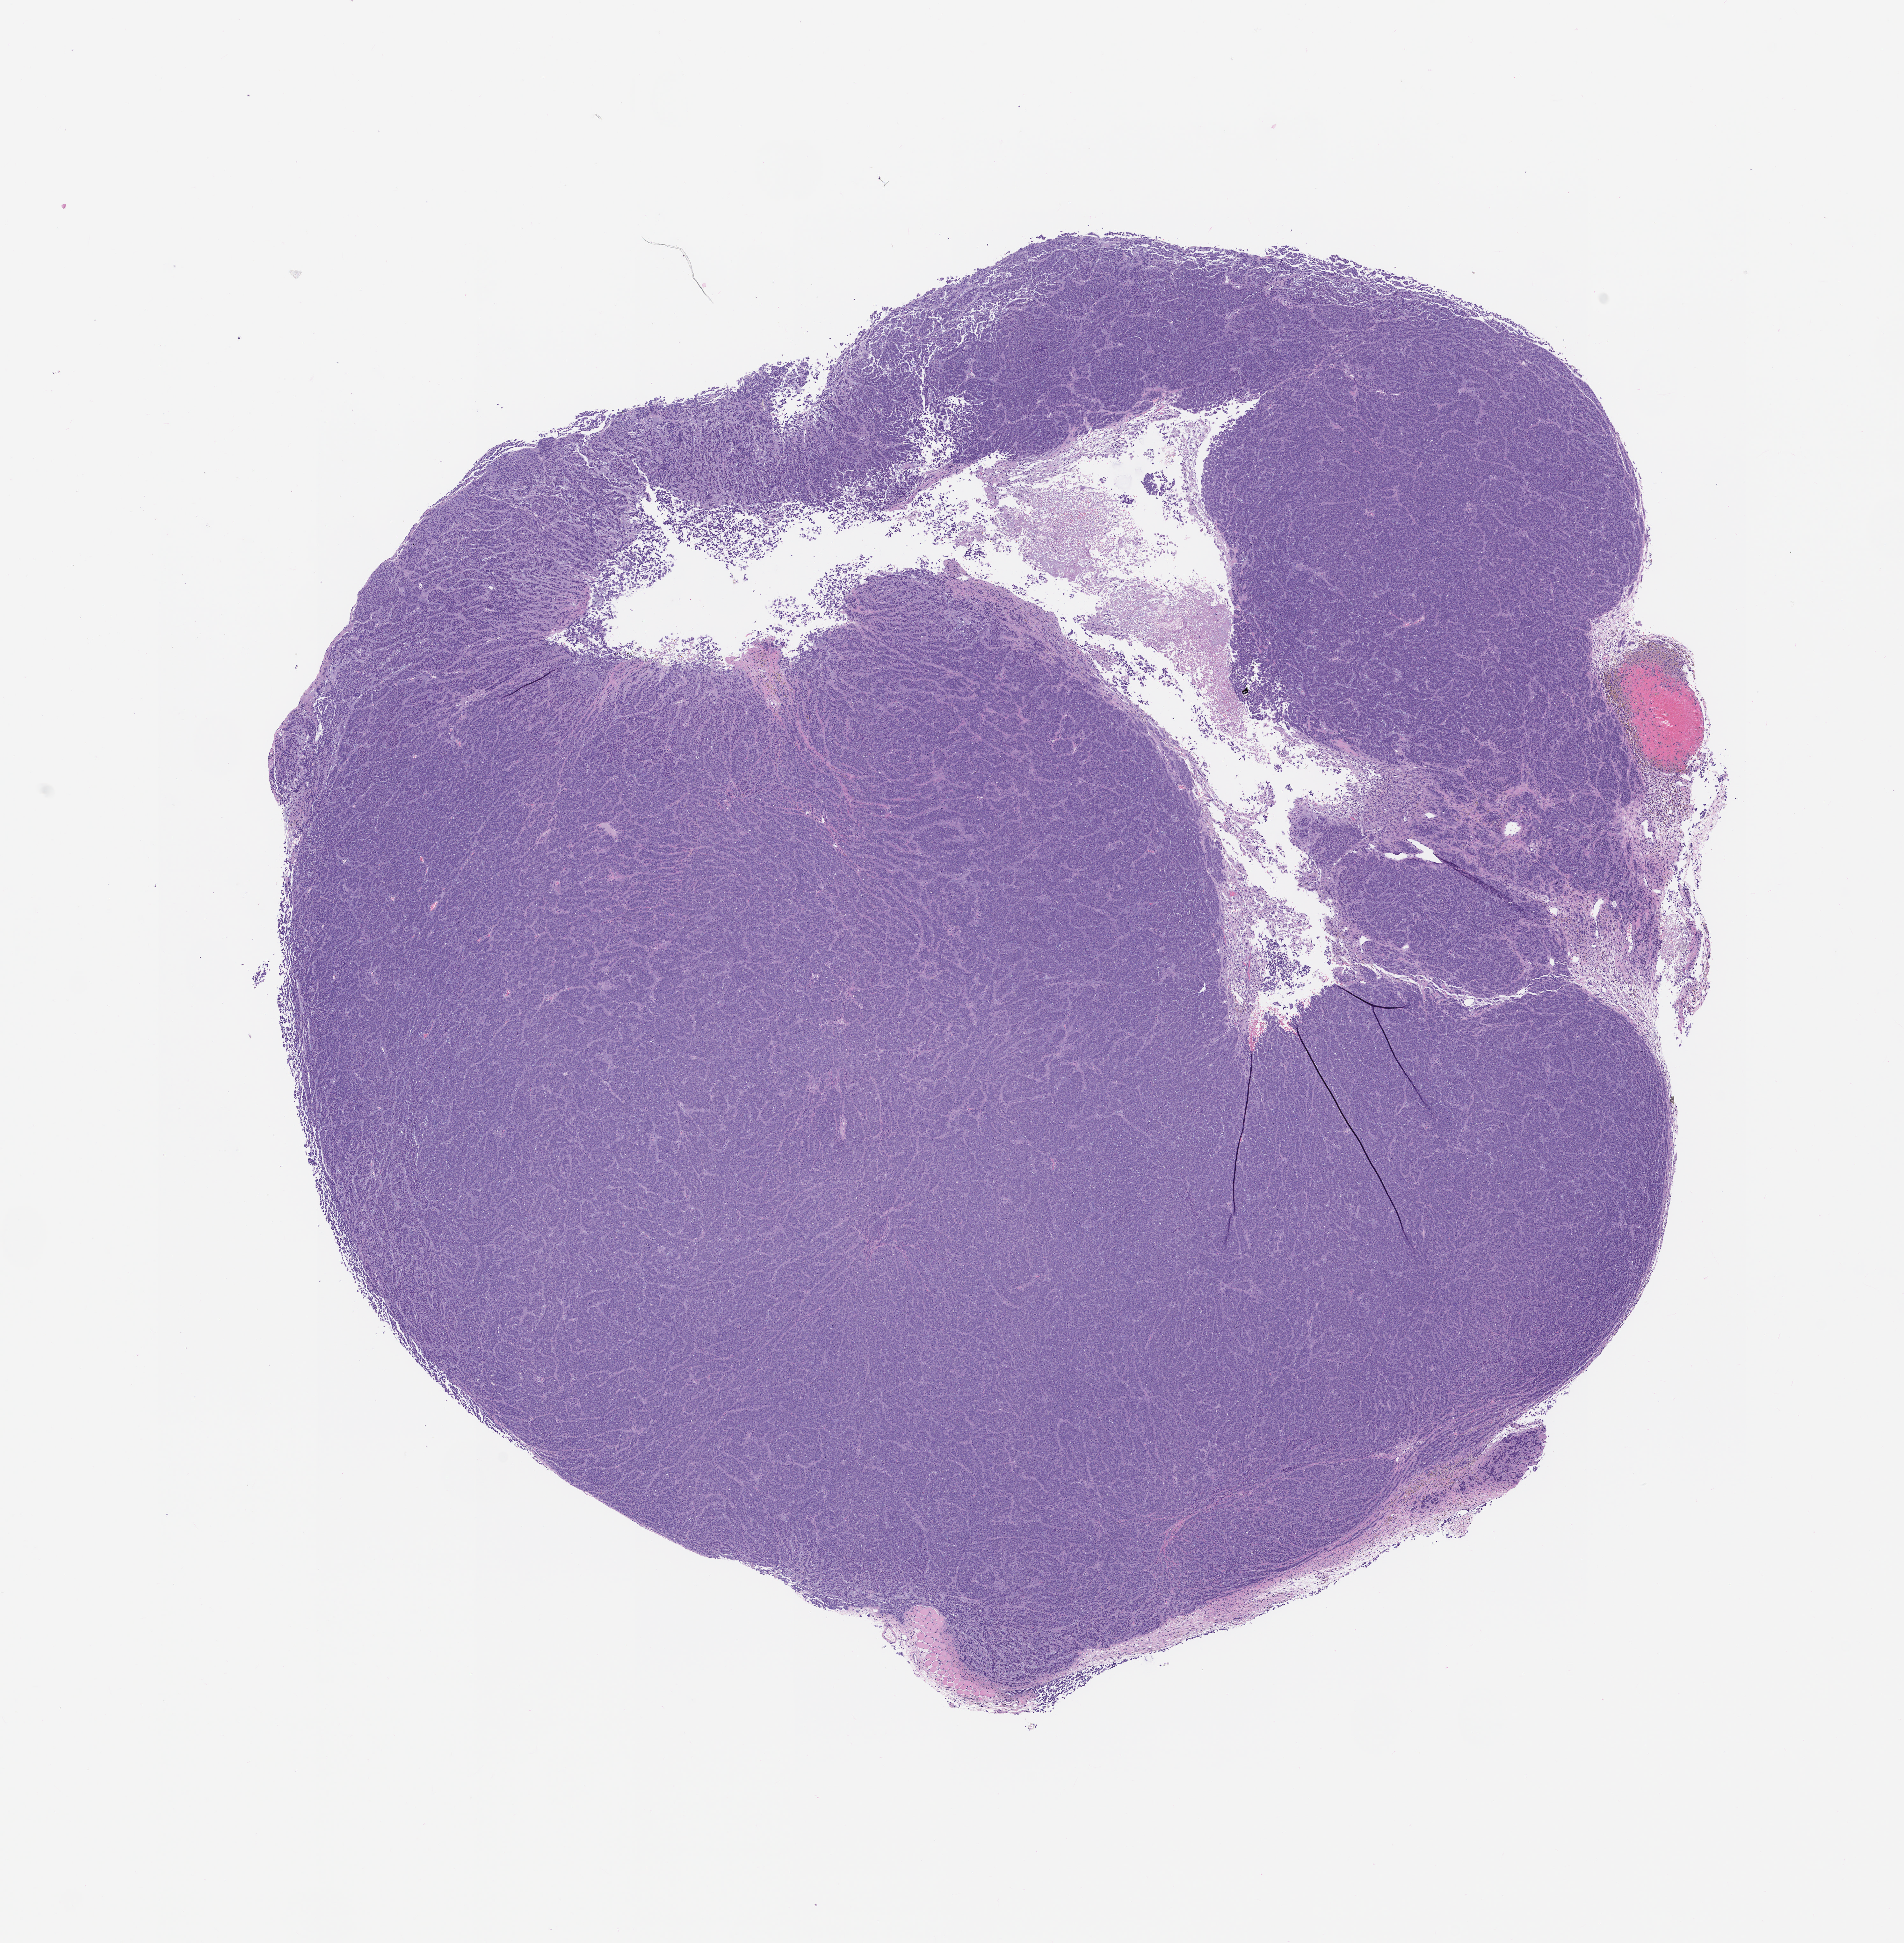
H&E whole-slide image of a patient-derived xenograft (PDX) tumor grown in a mouse, passage 2, a low-resolution overview of the entire scanned area, about 12.0 x 12.2 mm, FFPE section, originating tumor site category: ovary.
Originating patient diagnosis: Ovarian Carcinoma.